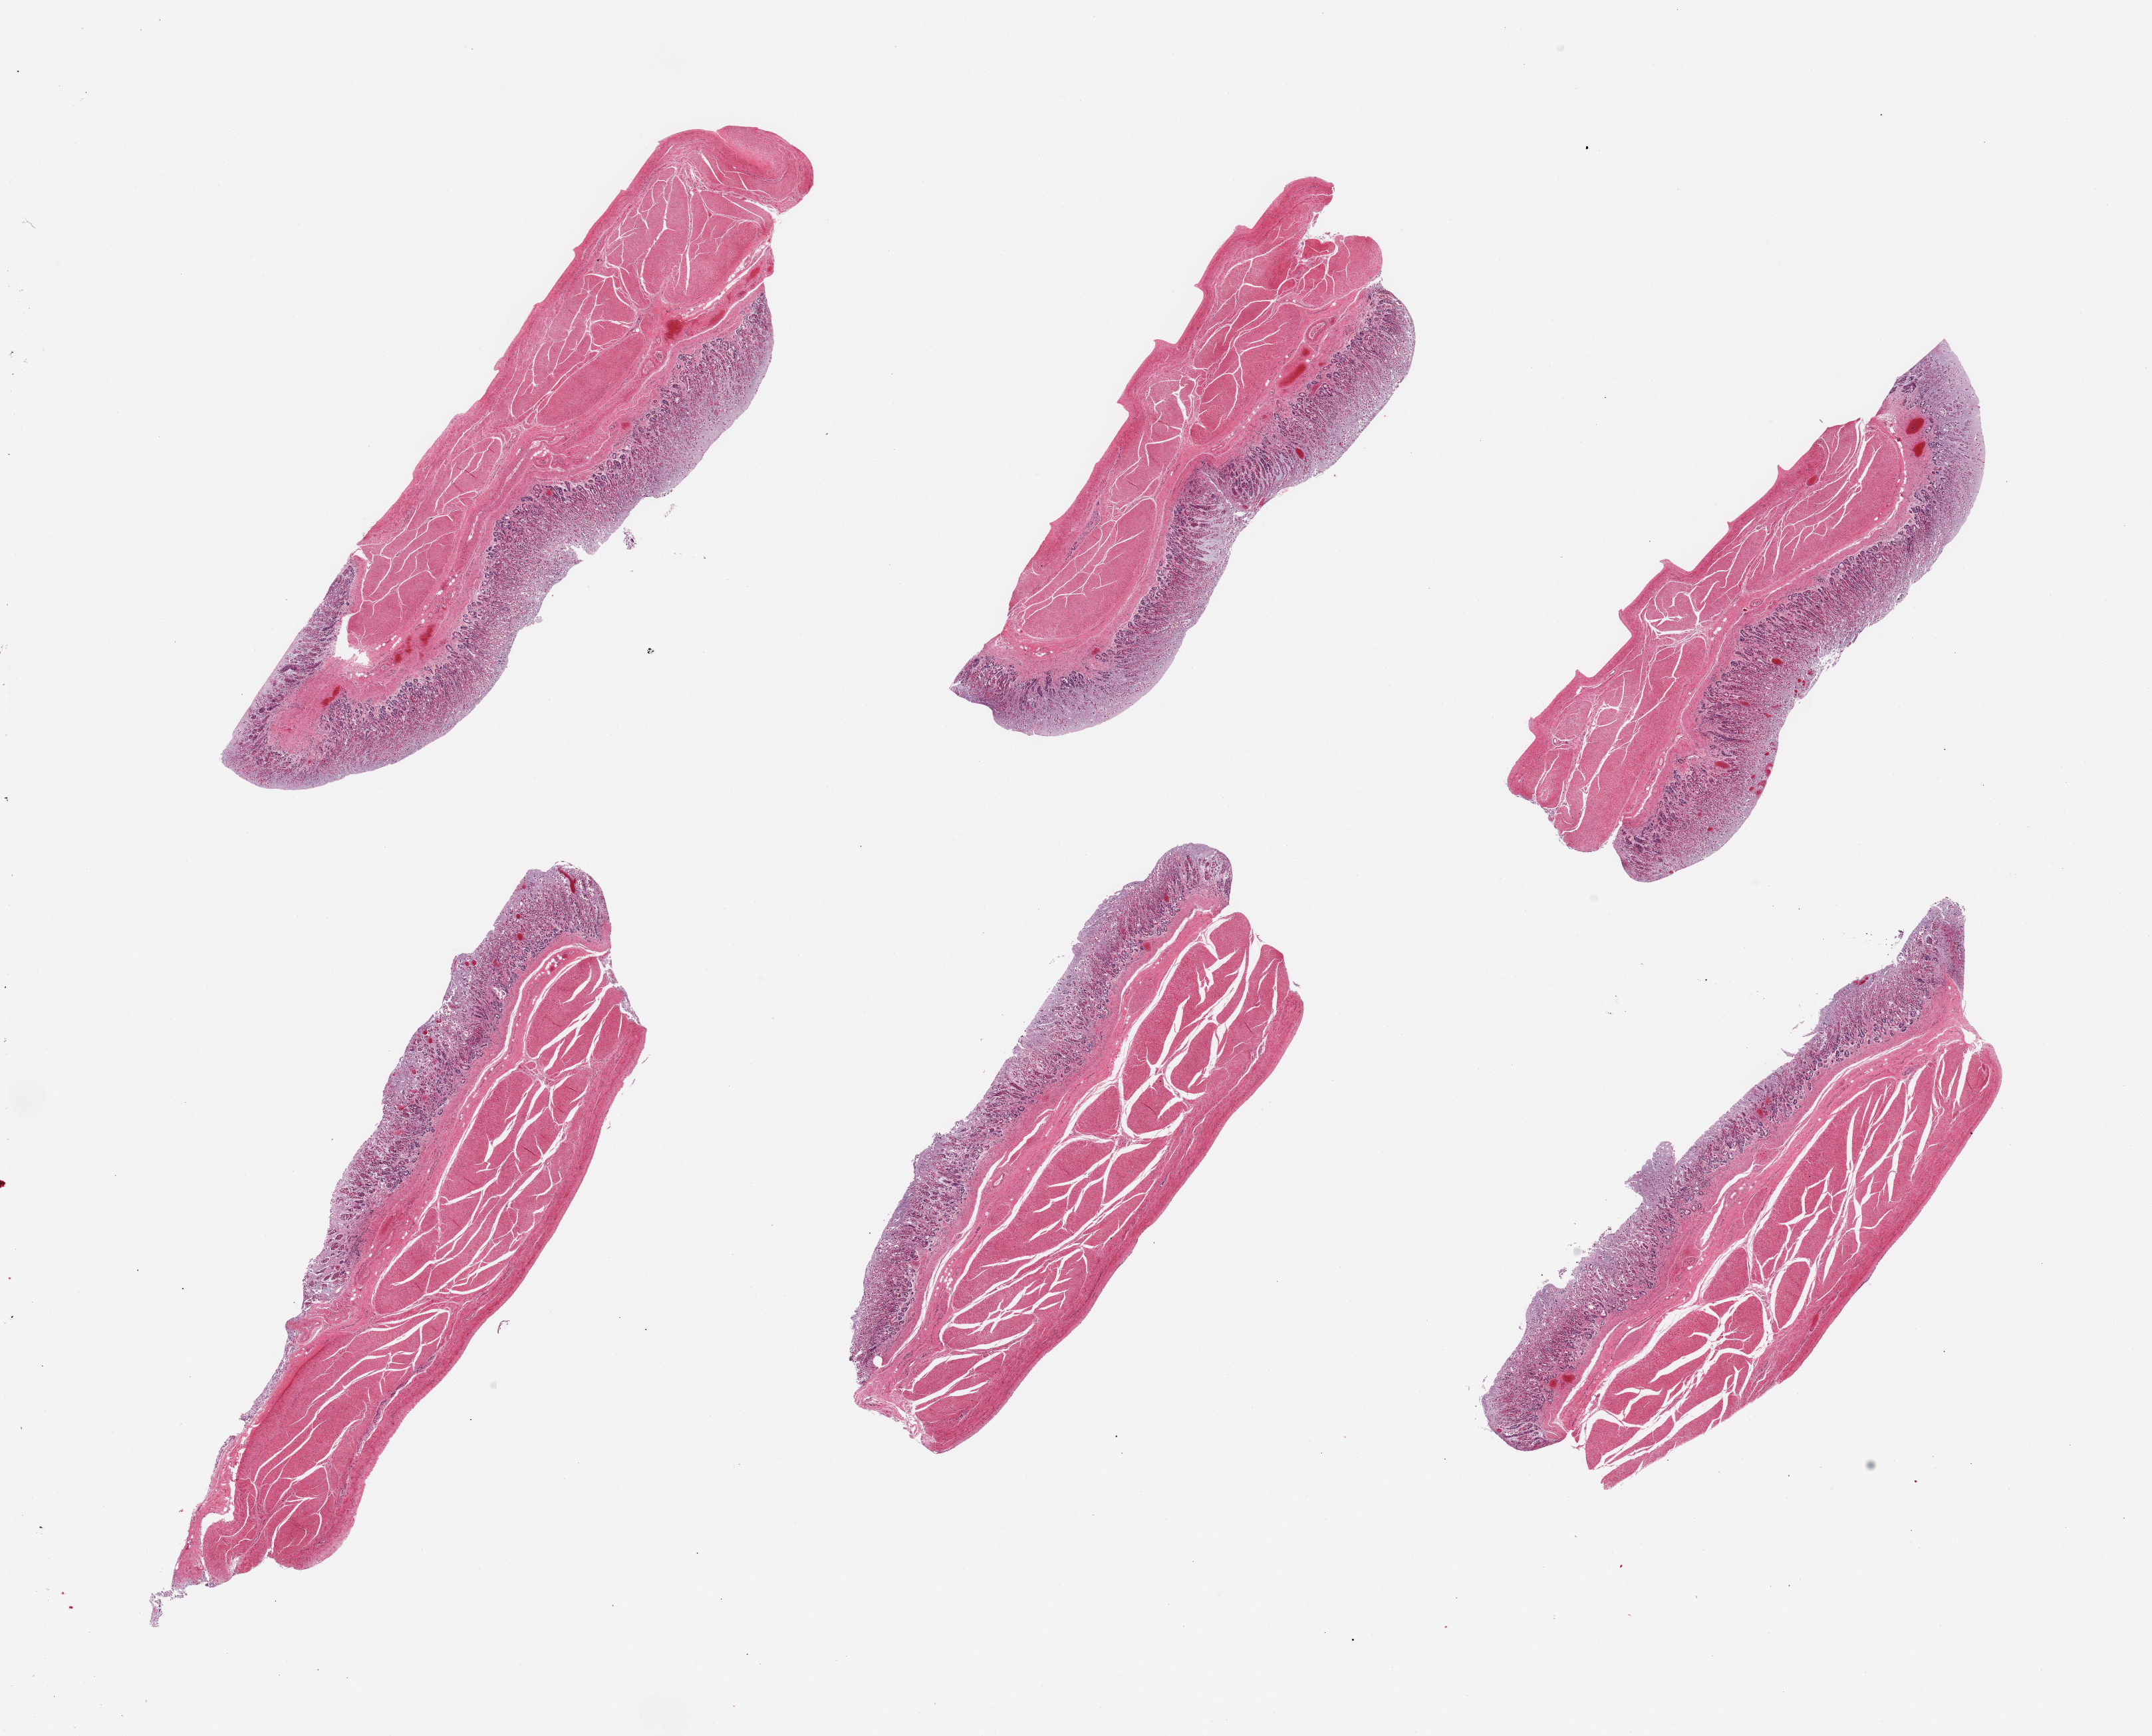
Digitized haematoxylin and eosin-stained section — a low-resolution overview of the entire scanned area, about 25.6 x 20.6 mm (acquisition: 20x scan); PAXgene-fixed paraffin-embedded (PFPE) section; target tissue: stomach; tissue donor sample. Donor sex: female.
• pathologist's review note for this sample: 6 pieces, mucosa upto ~0.8mm, ~30% thickness, moderately advance autolysis